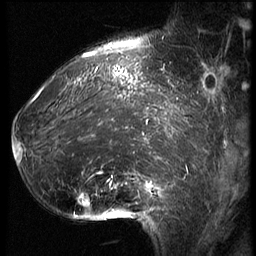
Breast MRI (dynamic contrast-enhanced), one sagittal slice; slice 19 of 62 in the series (ordered by position); 3 images stored at this slice position (order not interpretable as contrast timing); 1.5 T; TE 4.2 ms, TR 9 ms; 2.5 mm slice thickness; 256 × 256 image matrix. Patient: female, 39 years. Case-level facts recorded for this patient, not image findings: setting: breast cancer imaged before/during neoadjuvant chemotherapy; receptor status: HER2-positive.
Outlined on this slice (semi-automatic segmentation, software-assisted and operator-edited):
- analysis volume of interest (the breast-tissue region the enhancement analysis was run in; not a lesion): bounding box (x1, y1, x2, y2) in pixels: (16, 64, 171, 228)
- tumour enhancement mask (voxels above the 140 % enhancement threshold inside the analysis volume of interest): (16, 66, 171, 205)